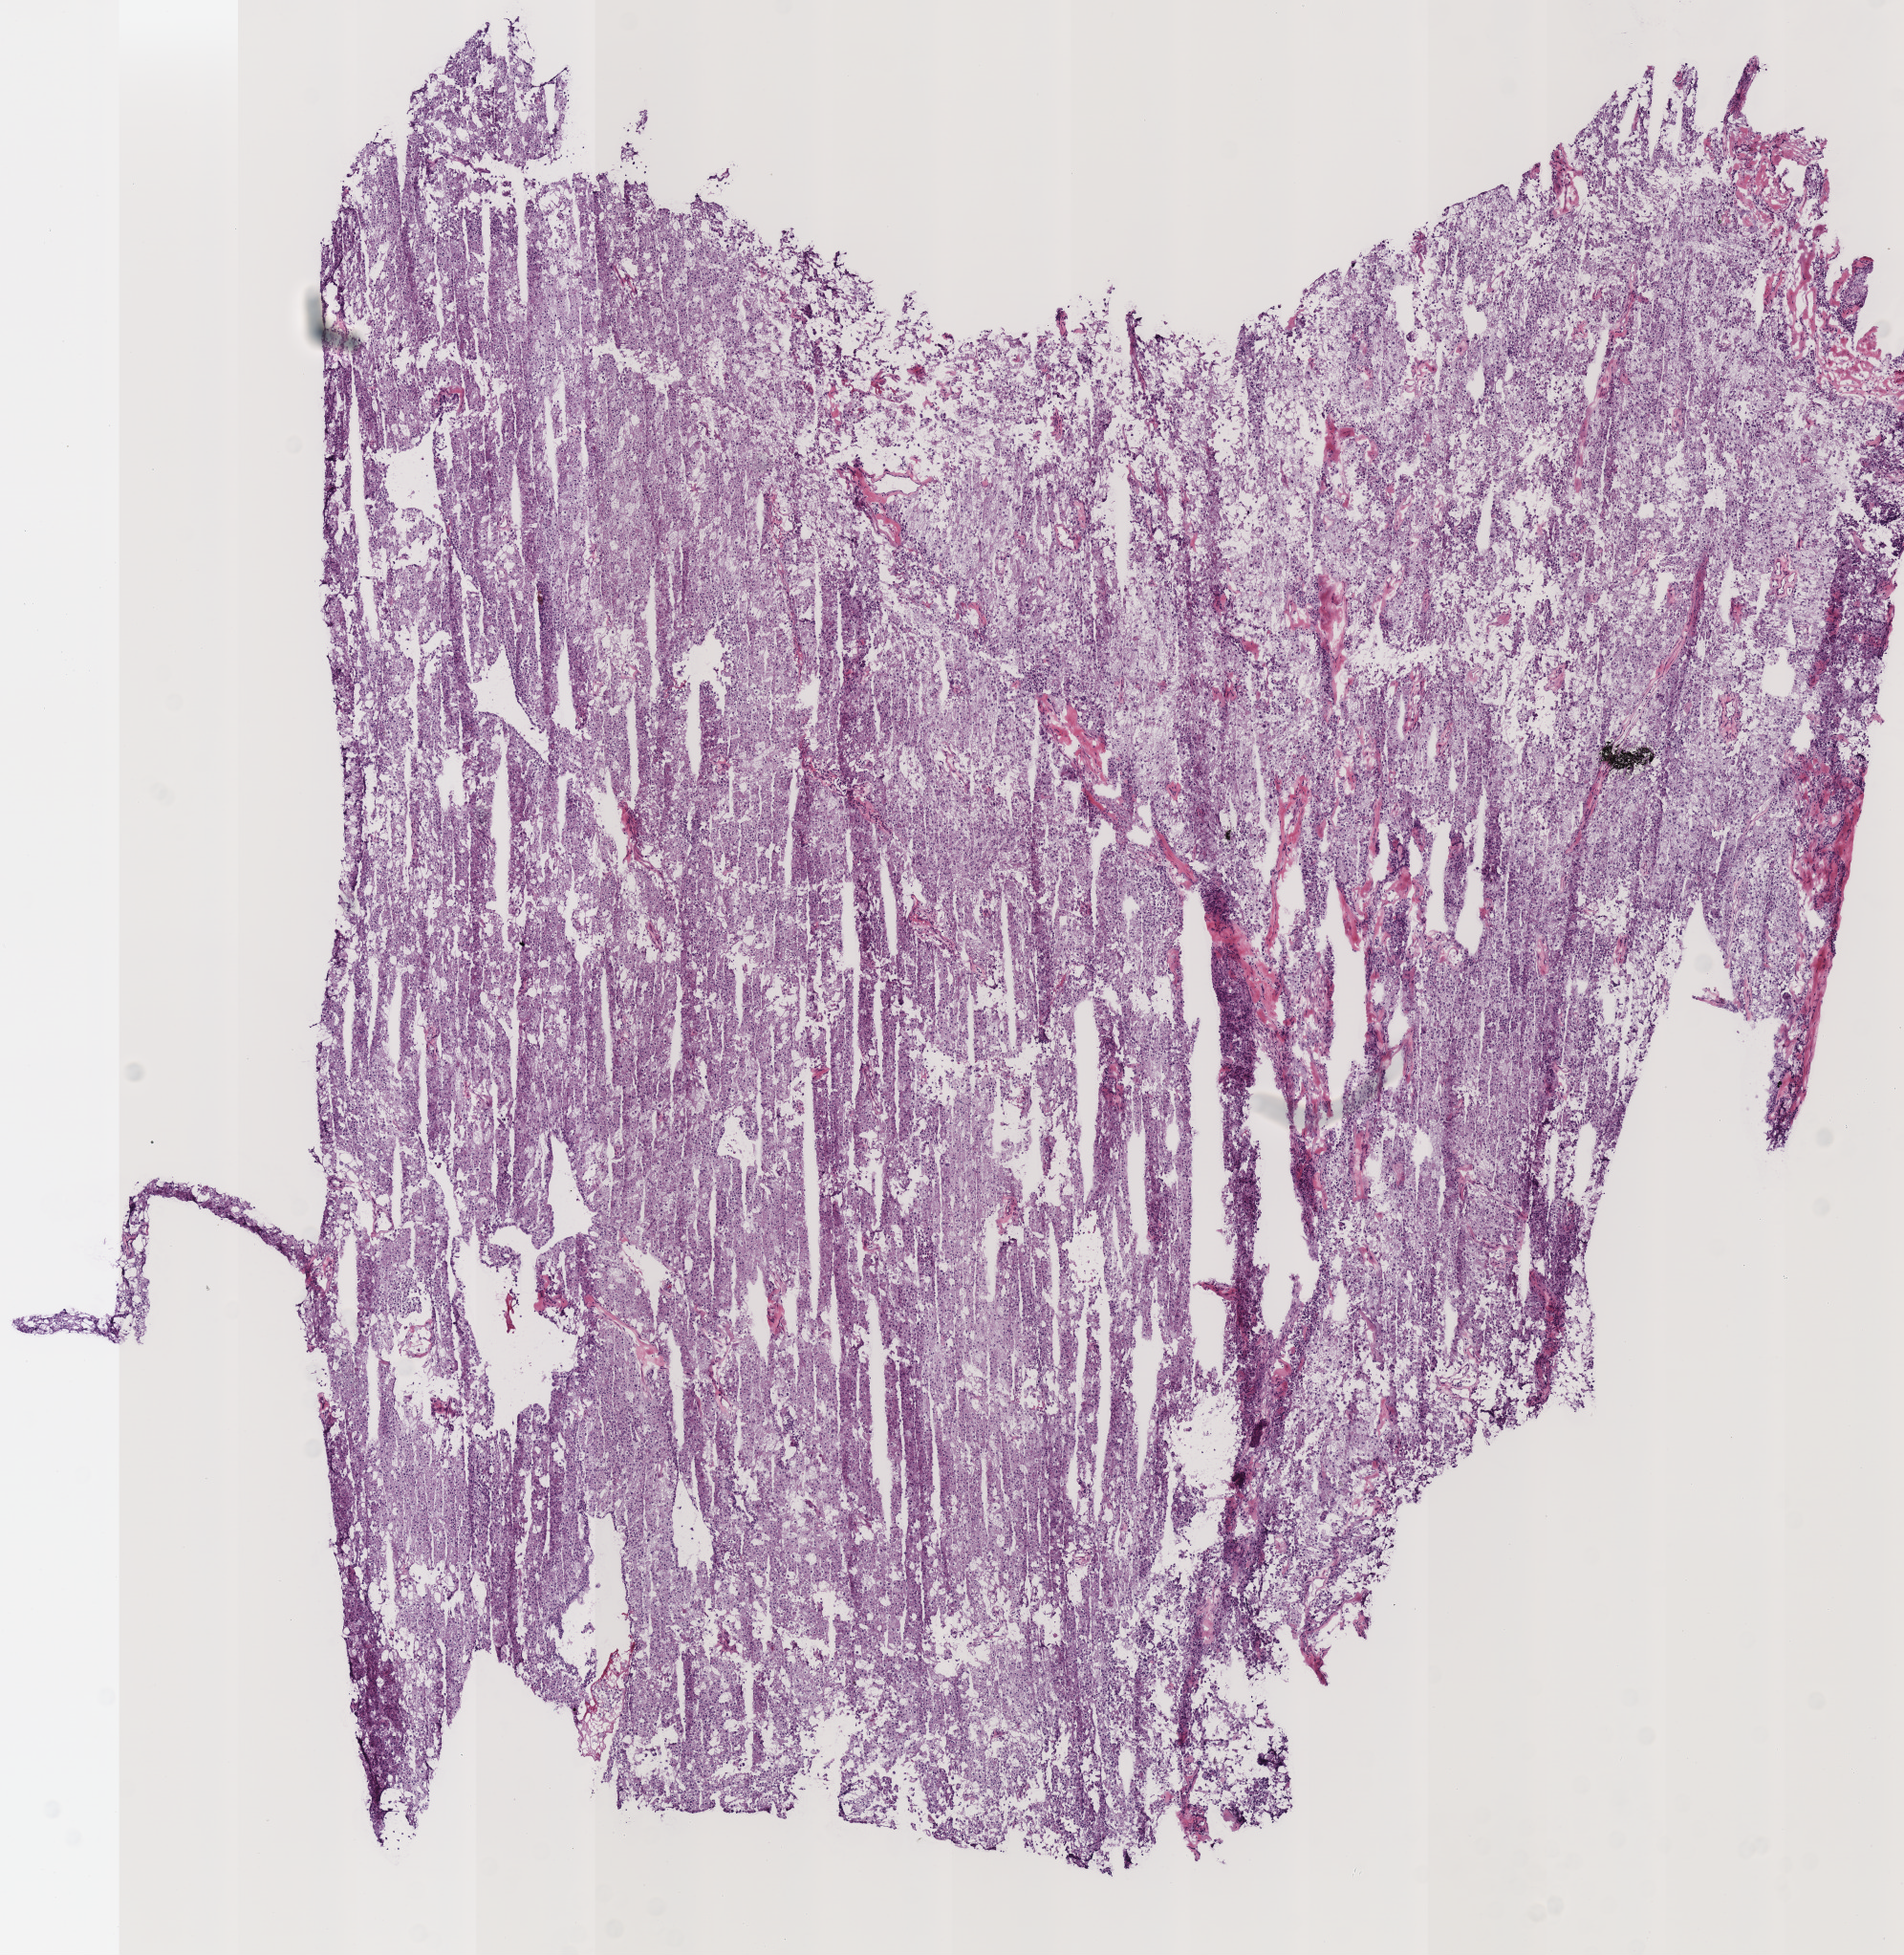
H&E whole-slide image, shown as a low-resolution overview of the whole scanned area (about 7.8 x 8.0 mm, acquisition: 40x scan), frozen section from the top of the tissue portion, sample: primary tumour, kidney. Female patient; age at initial diagnosis 50 years. Pathologist review of this section (percent, as recorded): tumour cells 100%, tumour nuclei 80%, normal cells 0%, stromal cells 0%, necrosis 0%. Infiltration values recorded for this section: lymphocyte infiltration 1%, monocyte infiltration 0%, neutrophil infiltration 0%.
AJCC pathologic stage: II (7th edition). Laterality: right. TNM: T2a NX MX. Pathologic diagnosis: Renal cell carcinoma, chromophobe type.